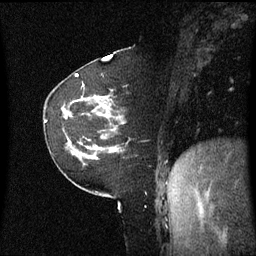
Breast MRI (dynamic contrast-enhanced), one sagittal slice. Position 19 of 60 along the scan axis. Dynamic contrast-enhanced series, image 2 of 3 at this slice position (ordered by acquisition). 1.5 T. TE 4.2 ms, TR 8.4 ms. 2.2 mm slice thickness. 256 × 256 image matrix, field of view 220 × 220 mm. Female patient, age 60 years. From the clinical record (not read from this slice): setting: breast cancer imaged before/during neoadjuvant chemotherapy; receptor status: triple-negative.
Structures marked on this image (semi-automatically segmented with operator editing):
- analysis volume of interest (the breast-tissue region the enhancement analysis was run in; not a lesion): box from (x=62, y=98) to (x=128, y=161) px
- tumour enhancement mask (voxels above the 70 % enhancement threshold inside the analysis volume of interest): (x=111, y=148)–(x=115, y=151)